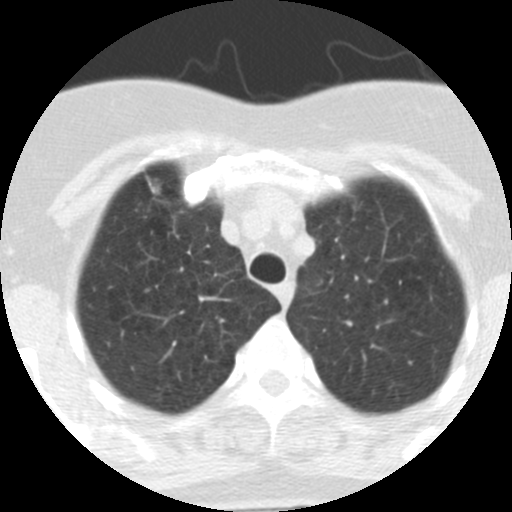
Low-dose screening chest CT, one axial slice. Reconstruction kernel STANDARD. 120 kVp. Lung window (W 1500 / L -600 HU). 512 × 512 image matrix, field of view 253 × 253 mm.
Annotated regions visible in this slice (expert manual segmentation):
- lesion 1 (tumor, upper lobe of right lung): bounding box [x1, y1, x2, y2] px = [148, 180, 158, 193]